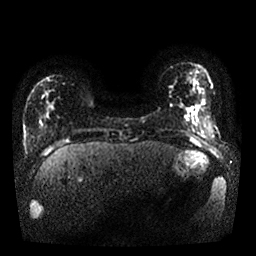
Breast MRI, one axial slice; position 4 of 25 along the scan axis; diffusion-weighted series; image 2 of 4 stored at this slice position (different b-values; order by instance number); 1.5 T; 4 mm slice thickness; 256 × 256 image matrix, field of view 340 × 340 mm. Female patient.
Structures marked on this image (manually delineated by an expert):
- tumour on diffusion-weighted imaging: bounding box (x1, y1, x2, y2) in pixels: (192, 105, 200, 115)